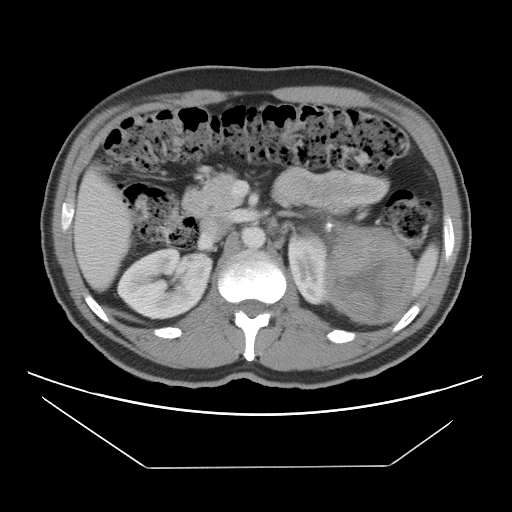
Contrast-enhanced abdominal CT, one axial slice. Position 66 of 131 along the scan axis. Soft-tissue window (W 400 / L 40 HU). 512 × 512 image matrix, field of view 396 × 396 mm. Patient: male, 44 years. From the clinical record (not read from this slice): diagnosis: adrenocortical carcinoma; tumour side: left adrenal; tumour size at pathology: 15.5 cm; Ki-67 index: 6 %; stage (as recorded): 2.
Outlined on this slice (semi-automatically segmented with operator editing):
- mass: bounding box <328,228,412,321> (left, top, right, bottom; pixels)